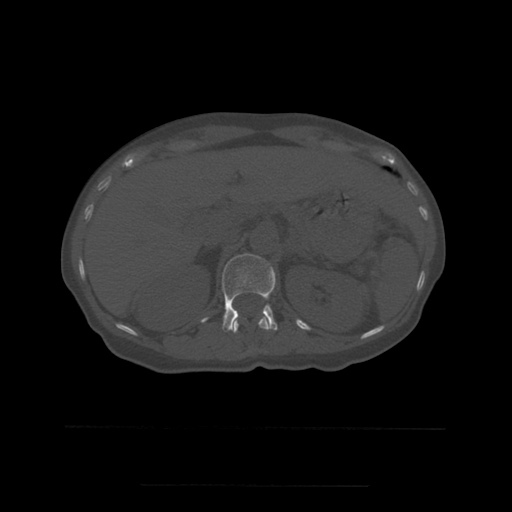
CT including the spine, one axial slice. Slice 244 of 544 in the series (ordered by position). Bone window (W 1800 / L 400 HU). 1.25 mm slice thickness. 512 × 512 image matrix, field of view 350 × 350 mm. Patient age 58 years. Case-level facts recorded for this patient, not image findings: primary cancer: lung.
Annotated regions visible in this slice (semi-automatically segmented with operator editing):
- L1 vertebra: bounding box (x1, y1, x2, y2) in pixels: (201, 254, 278, 333)
- T12 vertebra: (233, 317, 270, 333)